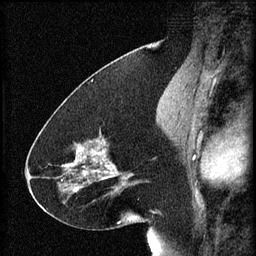
Breast MRI (dynamic contrast-enhanced), one sagittal slice. Slice 30 of 60 in the series (ordered by position). 3 images stored at this slice position (order not interpretable as contrast timing). 1.5 T. TE 4.2 ms, TR 8.2 ms. 2 mm slice thickness. 256 × 256 image matrix, field of view 180 × 180 mm. Female patient, age 41 years.
Annotated regions visible in this slice (semi-automatic segmentation, software-assisted and operator-edited):
- analysis volume of interest (the breast-tissue region the enhancement analysis was run in; not a lesion): box from (x=72, y=132) to (x=134, y=195) px
- tumour enhancement mask (voxels above the 70 % enhancement threshold inside the analysis volume of interest): (x=72, y=140)–(x=134, y=191)